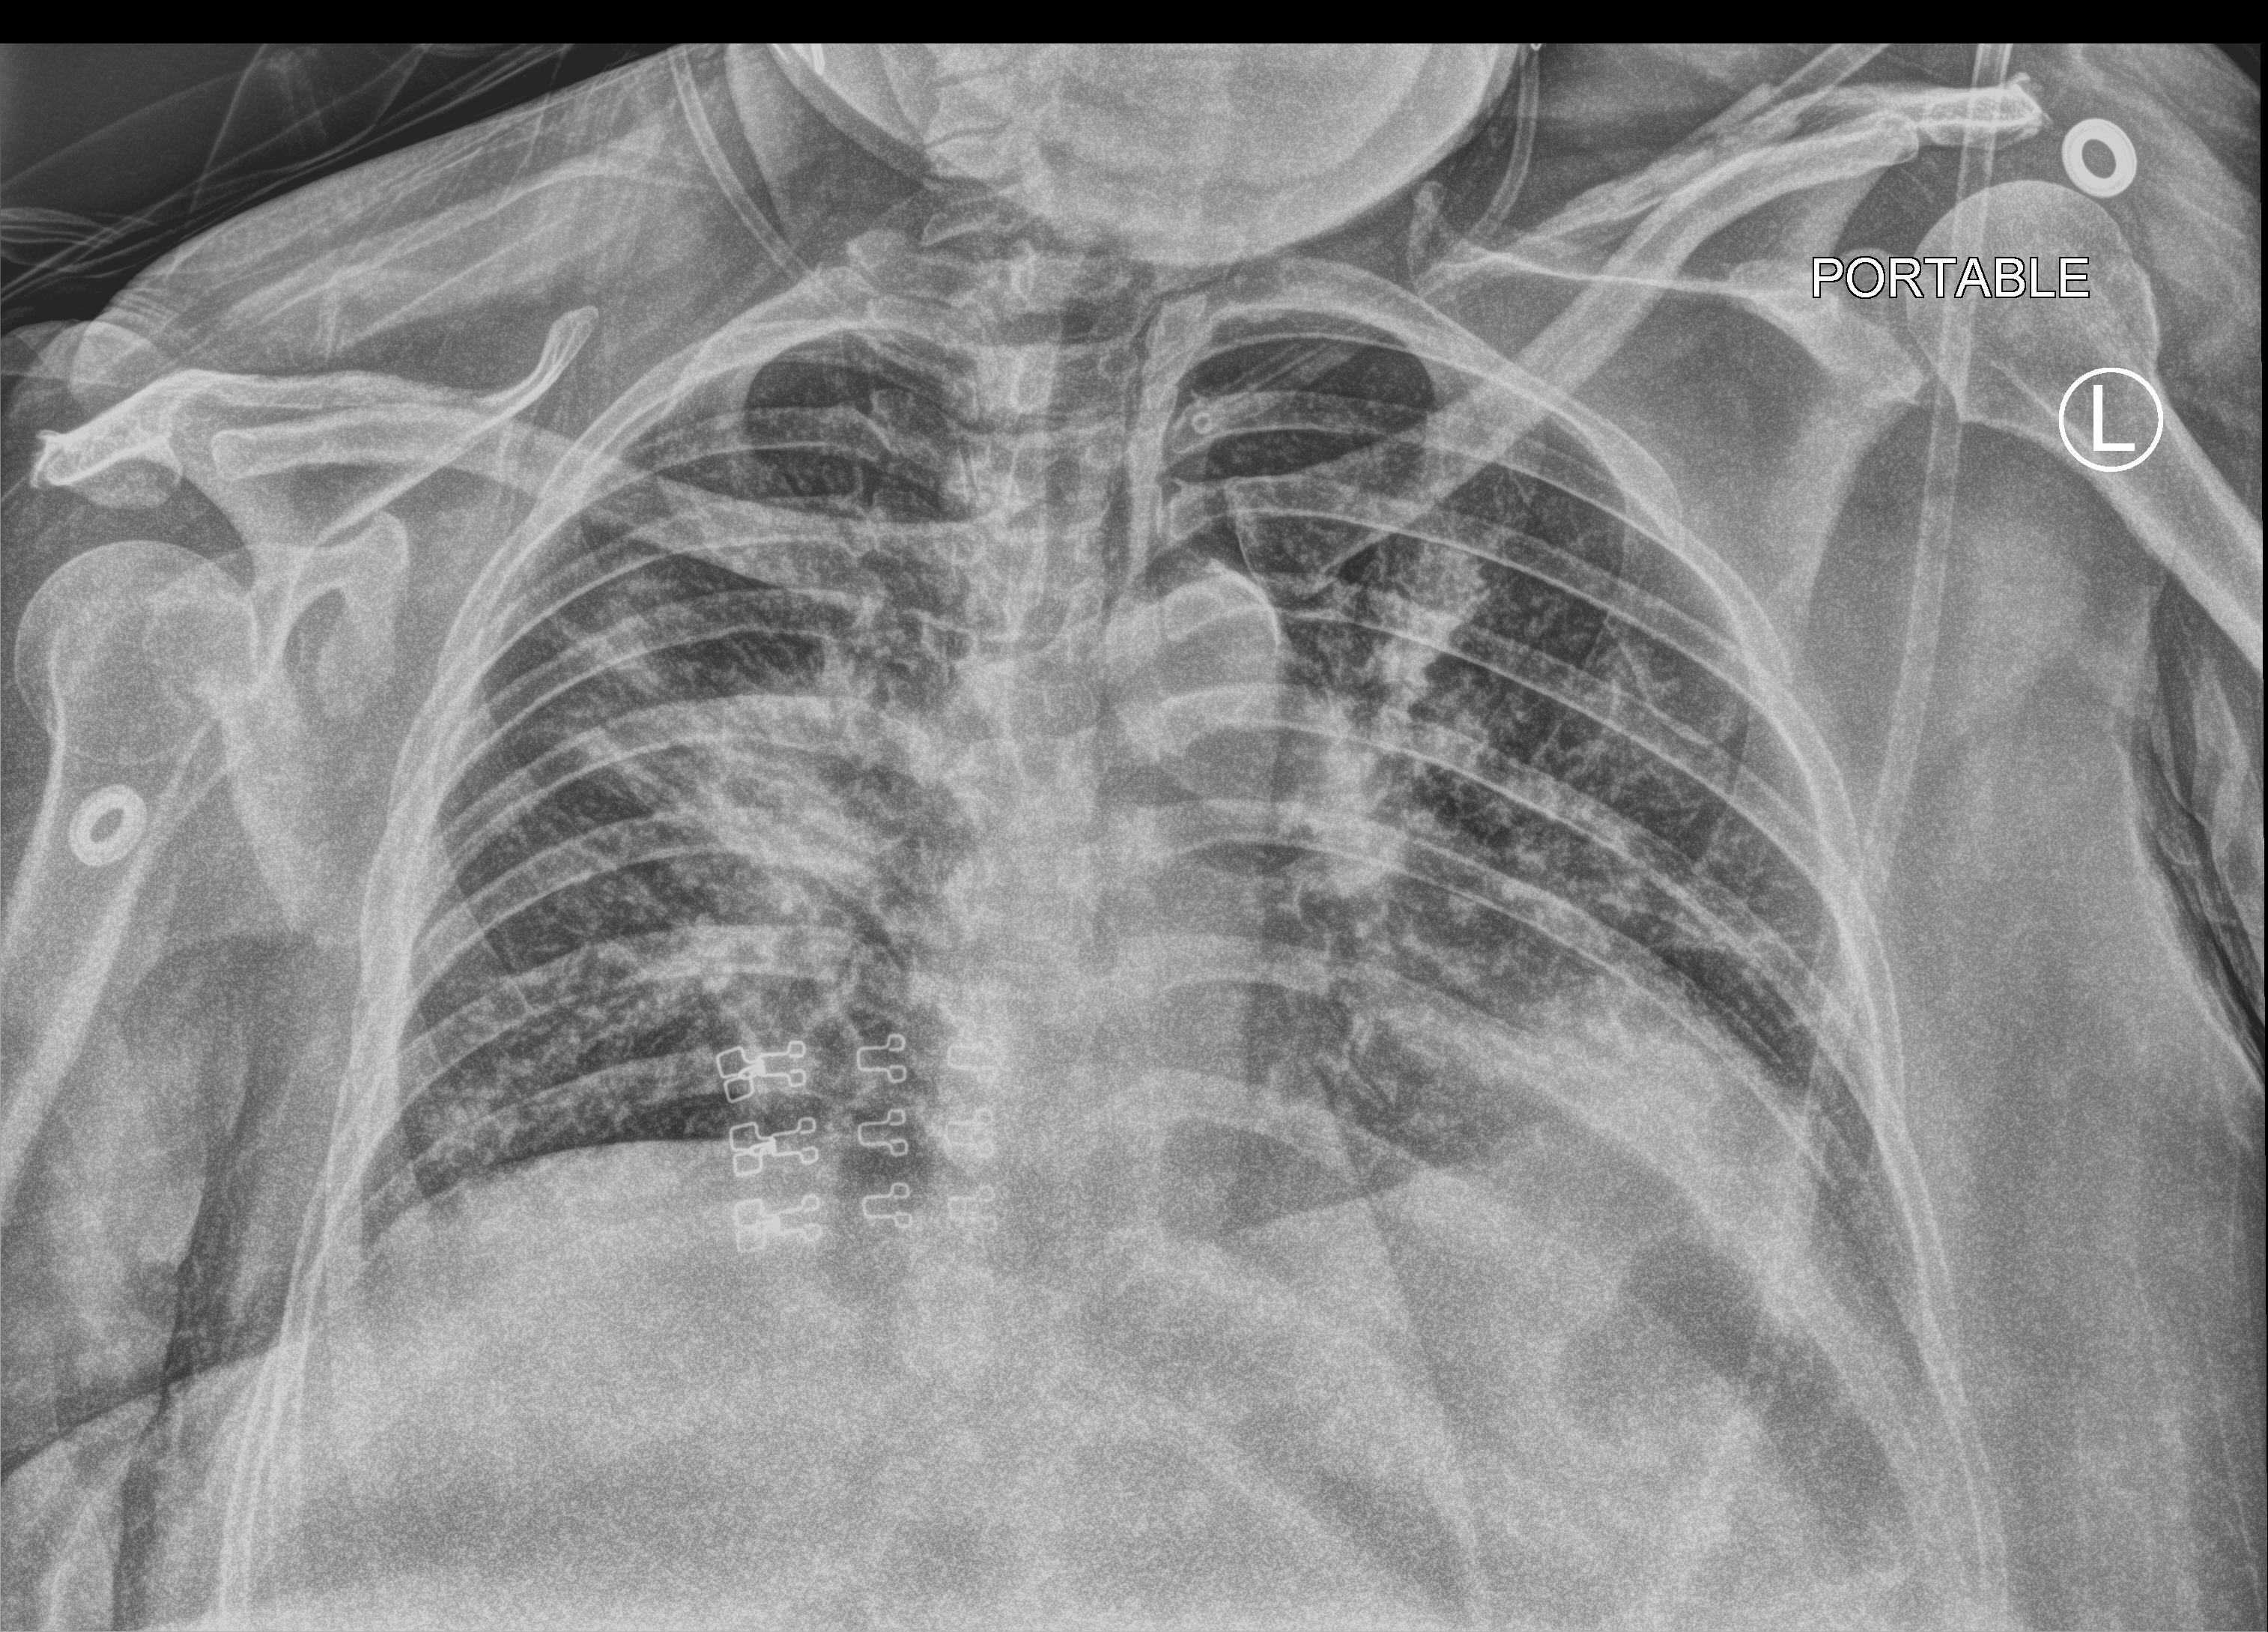
Chest X-ray (portable); anteroposterior (AP) projection. Patient hospitalised with COVID-19; female, aged 18–59 years.
Hospital-stay facts (about this admission, not read from this image; timing relative to this image not recorded):
- COPD (admission record): no
- mechanically ventilated during this hospital stay: no
- hypertension (admission record): yes